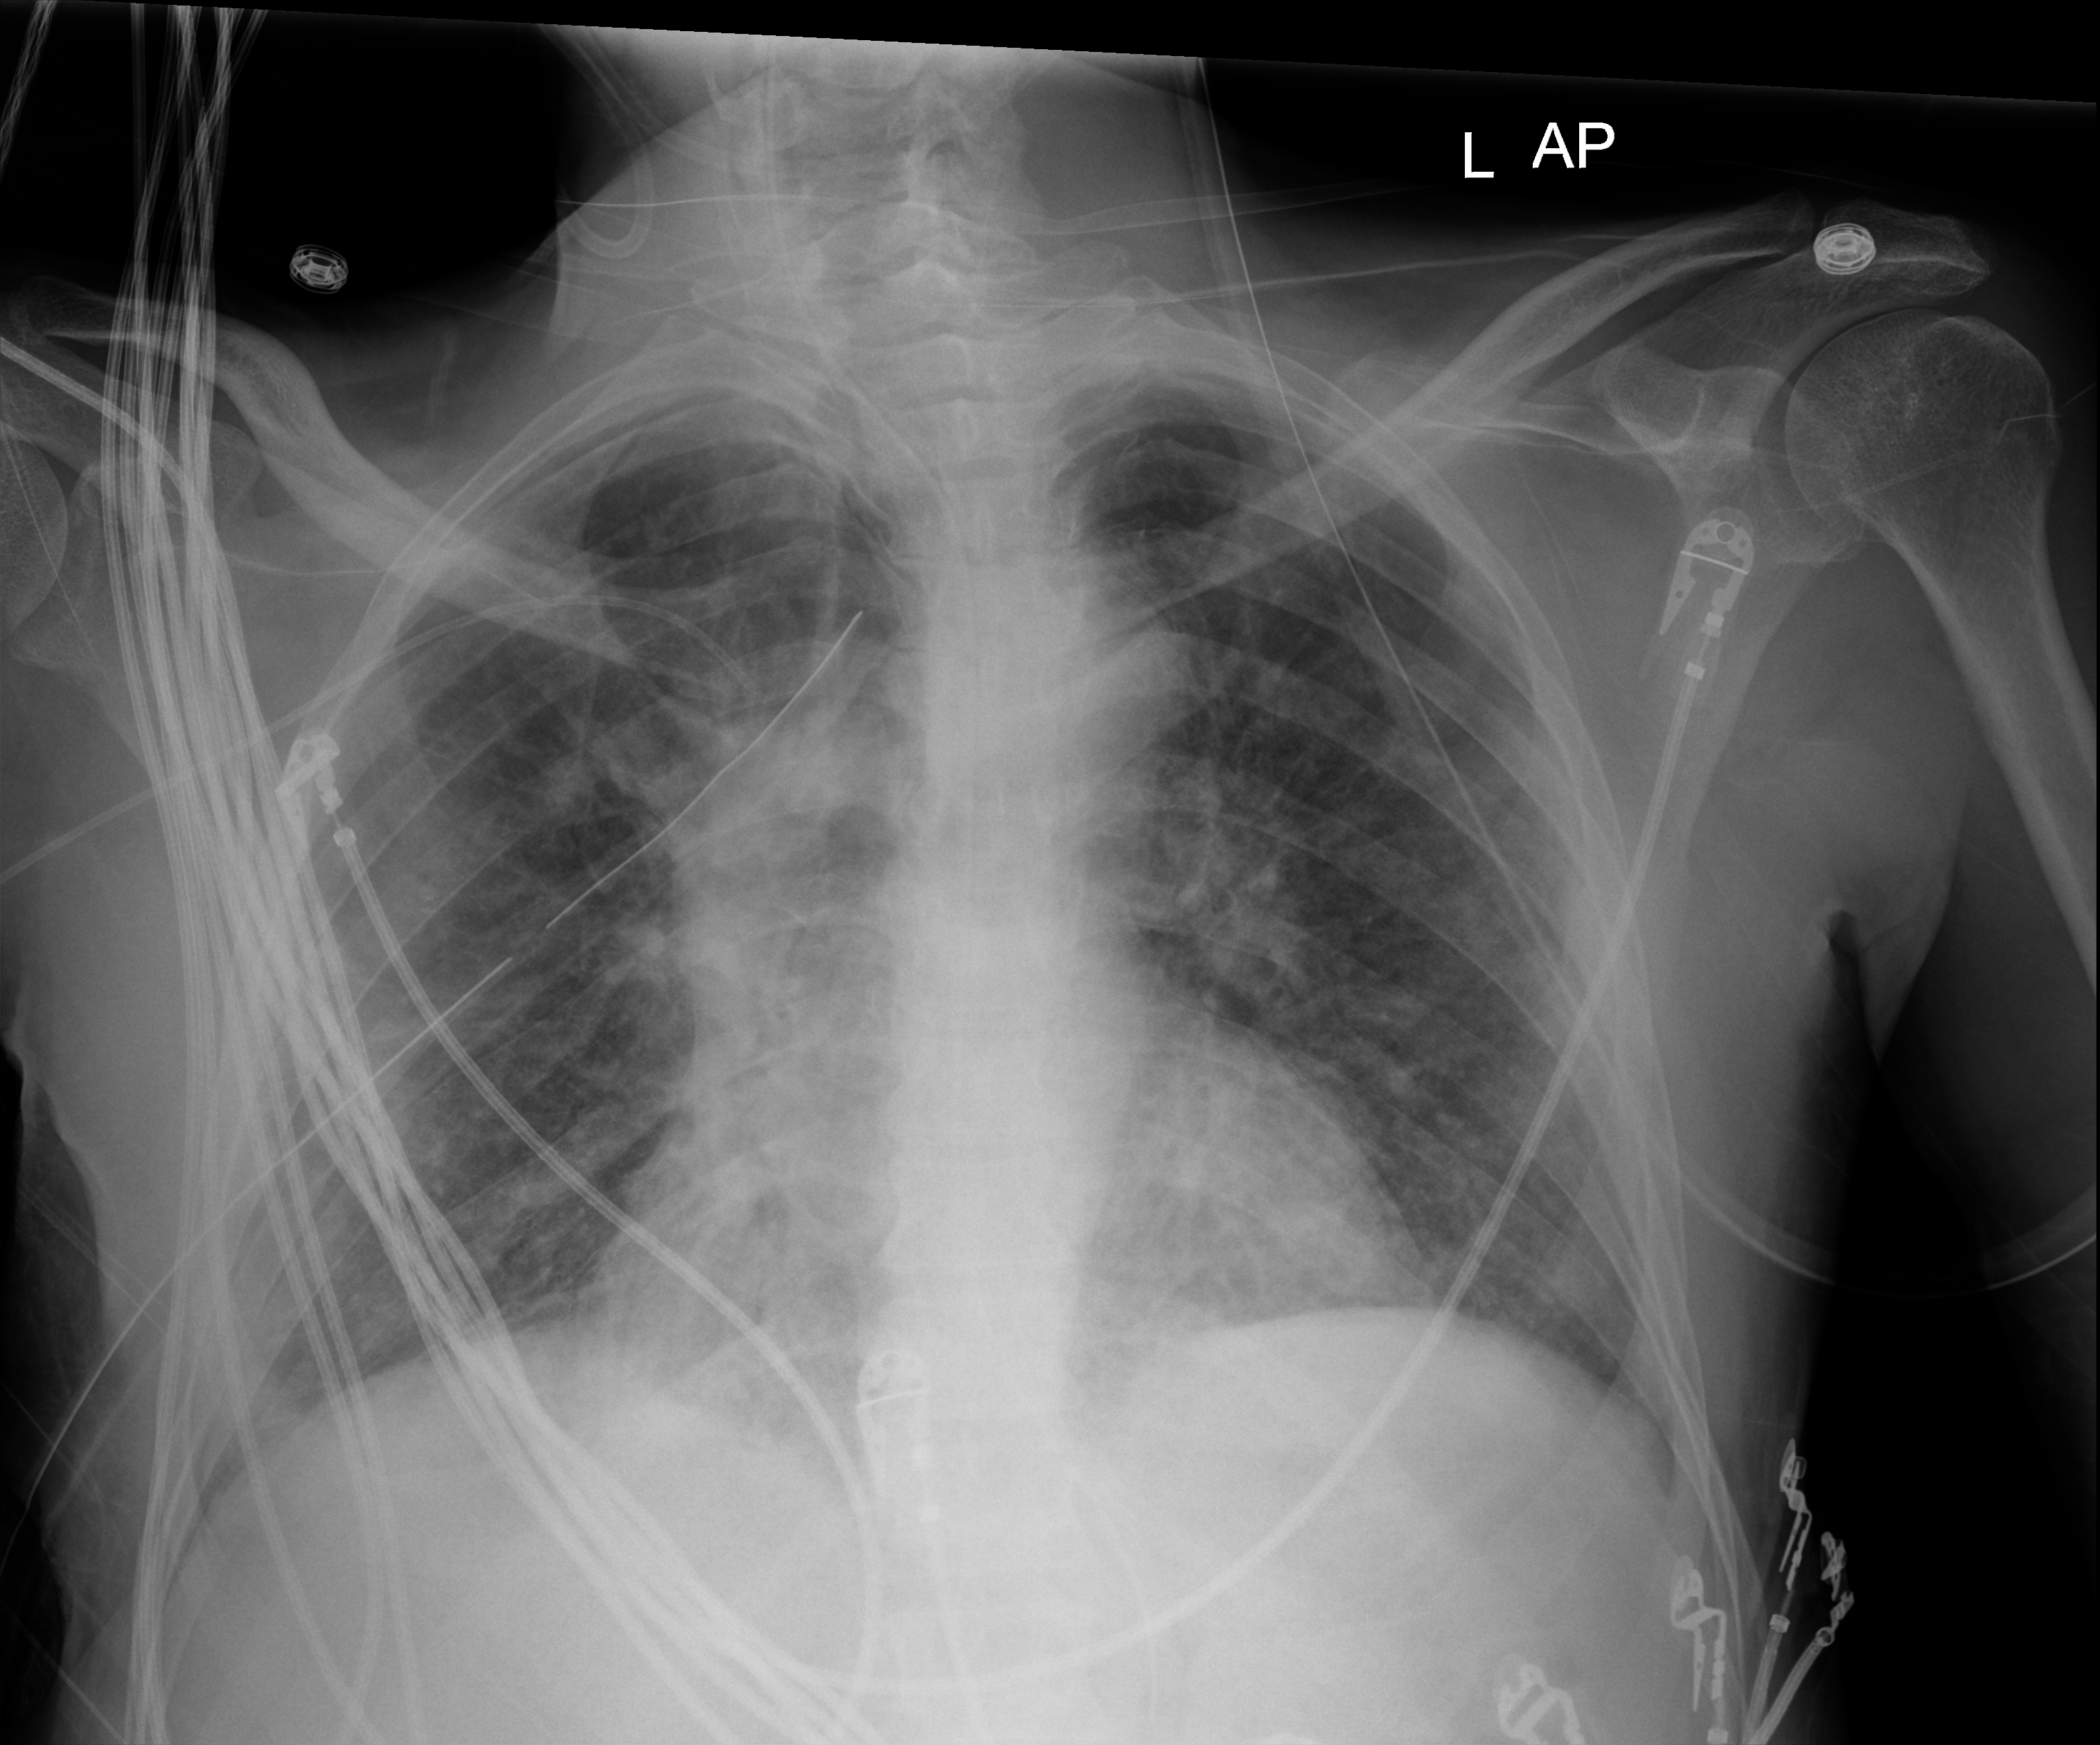
Portable chest radiograph, anteroposterior (AP) projection. Male patient hospitalised with COVID-19, age 18–59 years.
Hospital-stay facts (about this admission, not read from this image; timing relative to this image not recorded):
- mechanically ventilated during this hospital stay: yes
- admitted to intensive care during this hospital stay: yes